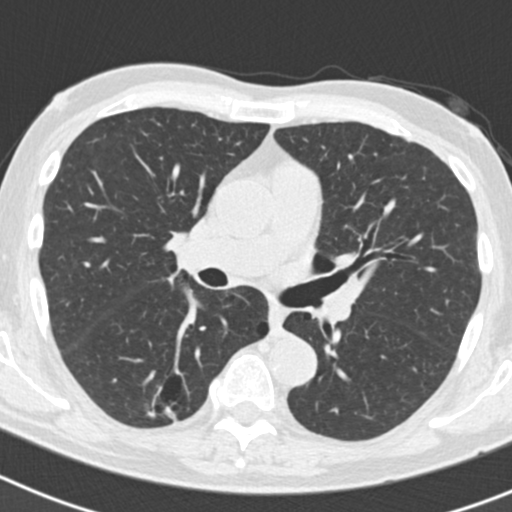
Axial slice from a low-dose chest CT screening exam, second annual screen, lung window (W 1500 / L -600 HU), slice 76 of 186 in the series, 512 × 512 image matrix. Male participant, aged 70 years at enrolment.
- Expert reader's lesion annotation, bounding box <133,375,198,433> (left, top, right, bottom; pixels).
- The screening reader recorded 5 non-calcified nodules or masses ≥4 mm on this exam (right lower lobe, right lower lobe, right upper lobe, right upper lobe, left upper lobe); which of them this box marks is not recorded.
- Official screen result: positive, other.
- Later outcome: lung cancer diagnosed 622 days after this screen (after the third annual screen) — bronchiolo-alveolar adenocarcinoma, NOS, right lower lobe, poorly differentiated (G3), stage IB (AJCC 6th edition), 30 mm at pathology.